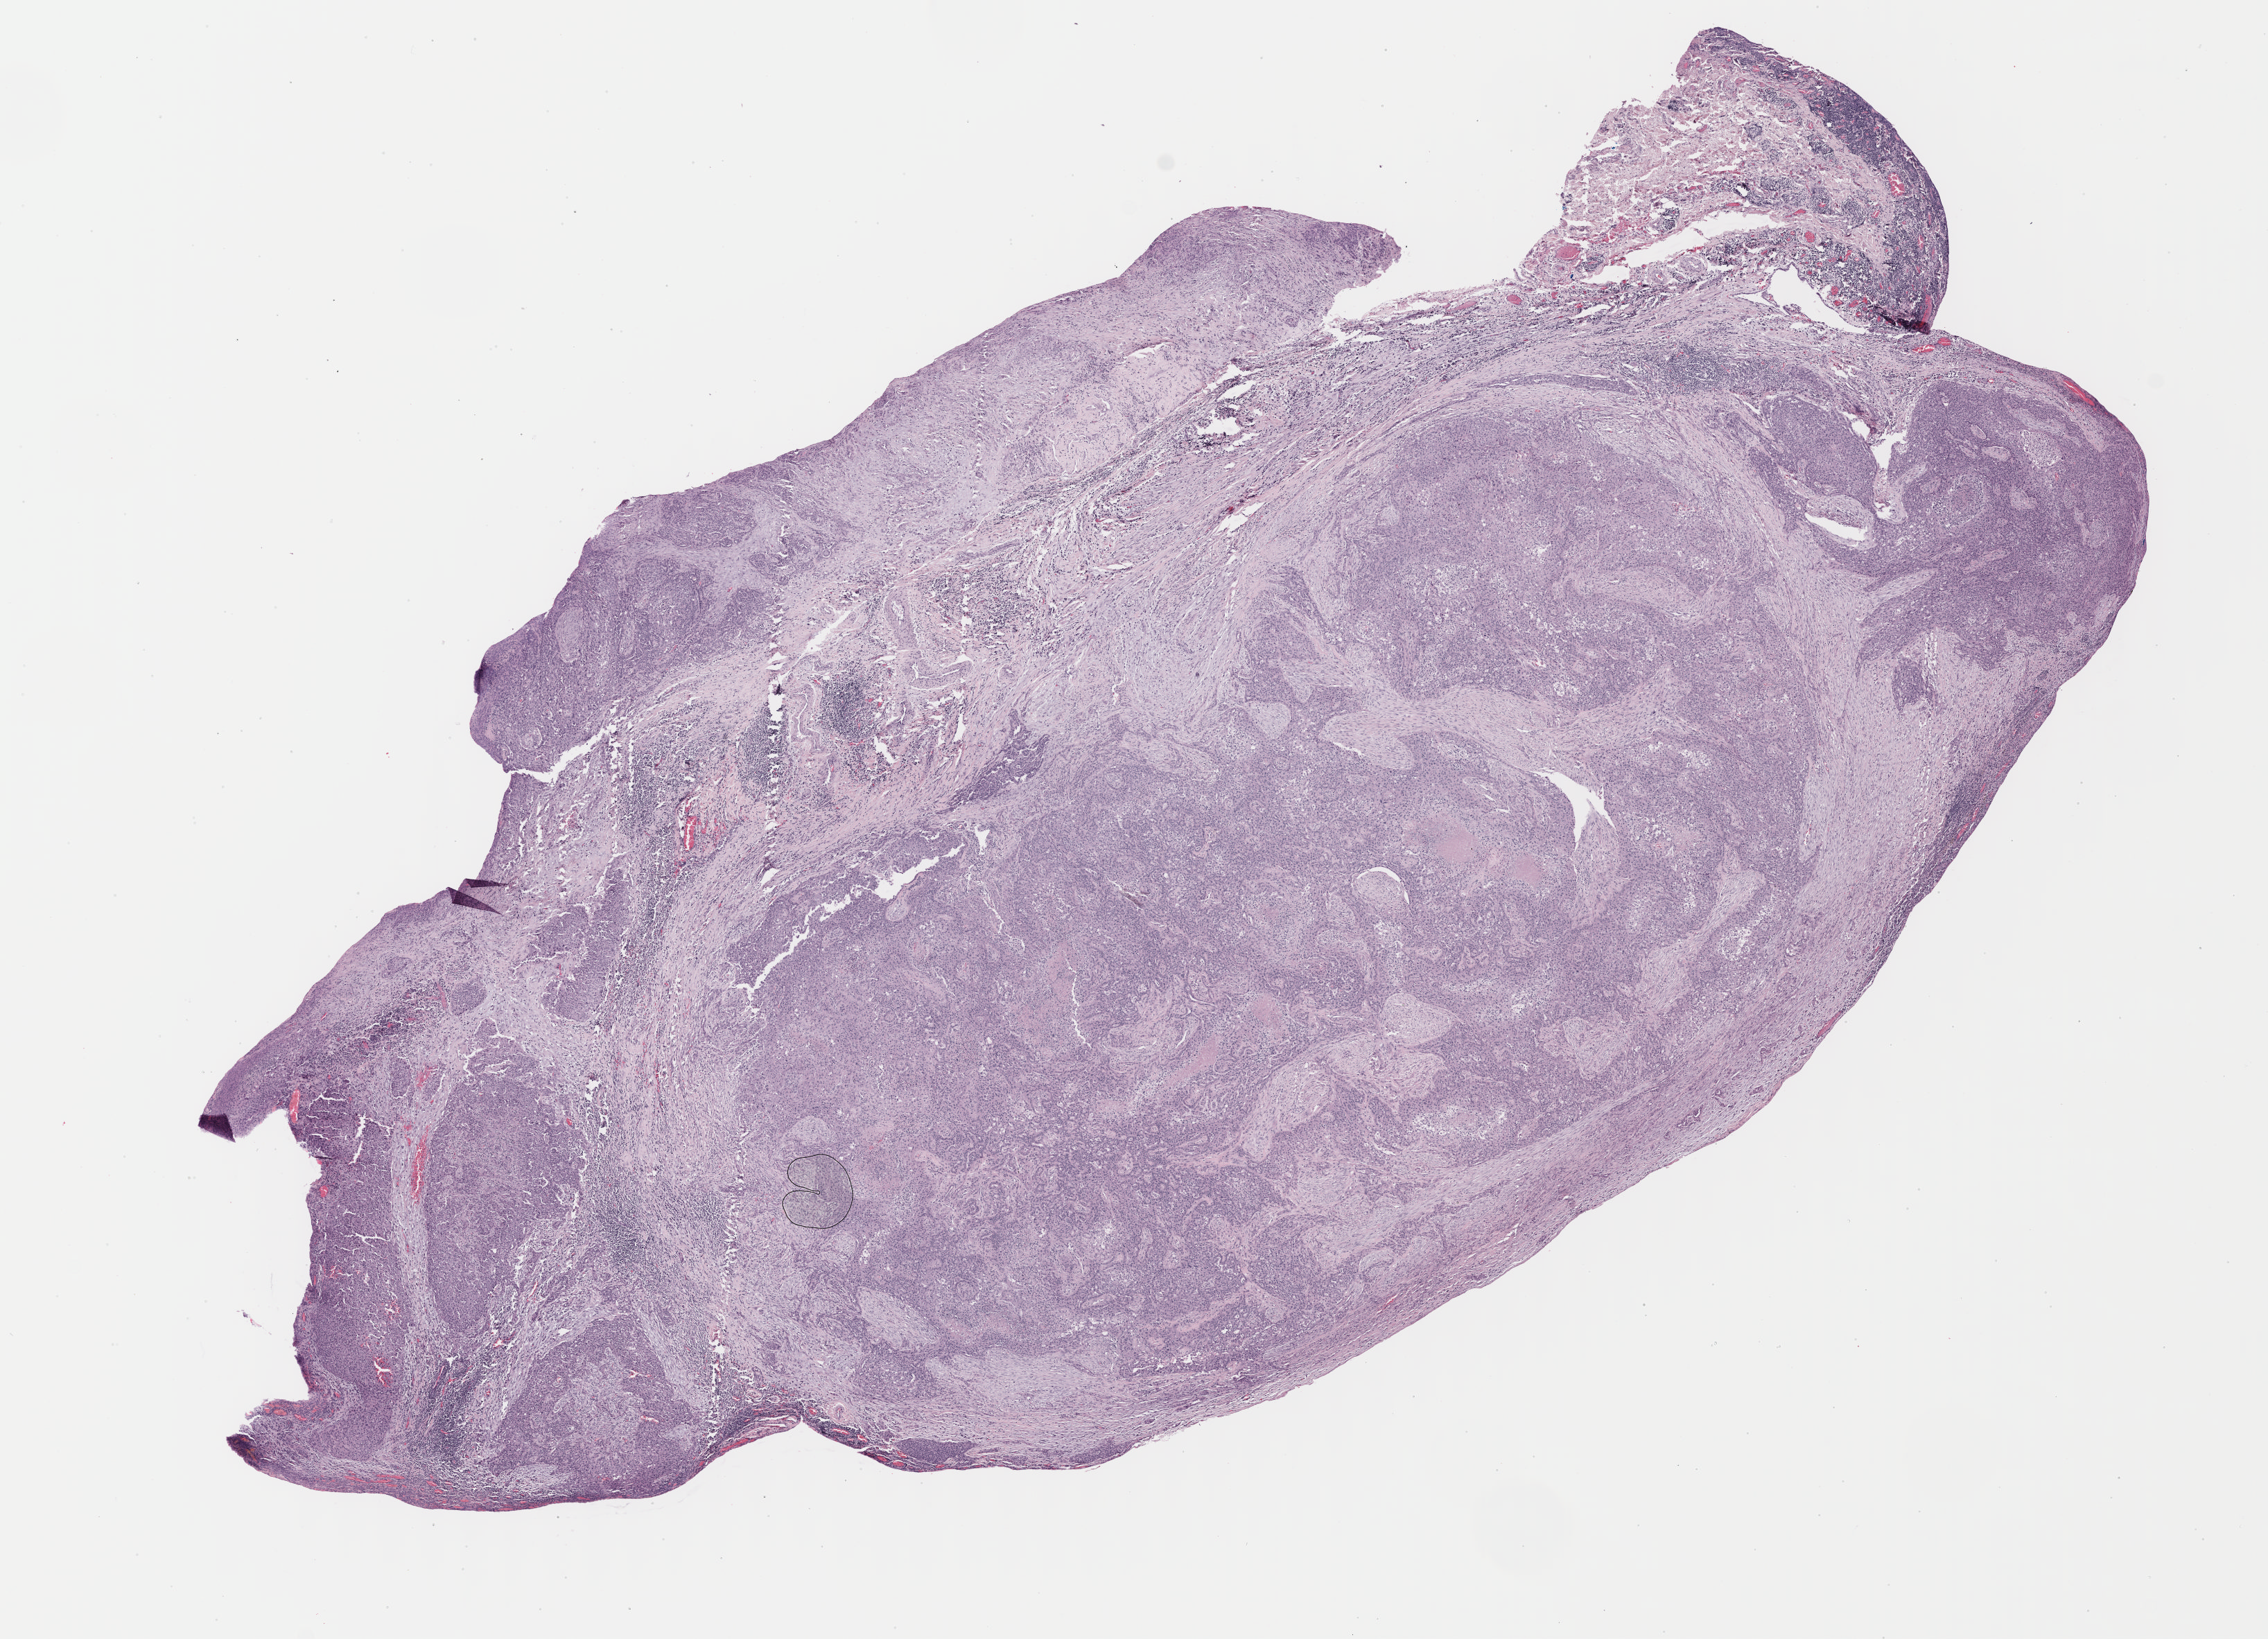
Whole-slide histology image, H&E-stained — a low-resolution overview of the entire scanned area, about 12.9 x 9.3 mm (slide scanned at 40x); formalin-fixed paraffin-embedded (FFPE) diagnostic section; sample: primary tumour, mesothelium. Female patient; age at initial diagnosis 55 years.
AJCC pathologic stage: III (6th edition). Diagnosis: Epithelioid mesothelioma, malignant (pleura, NOS). Laterality: left.